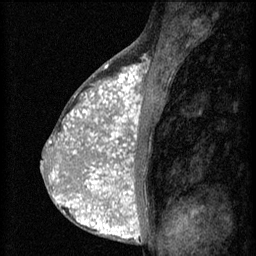
Breast MRI (dynamic contrast-enhanced), one sagittal slice. 3 images stored at this slice position (order not interpretable as contrast timing). 1.5 T. TE 4.2 ms, TR 8.2 ms. 2 mm slice thickness. 256 × 256 image matrix. Female patient, age 38 years.
Outlined on this slice (semi-automatically segmented with operator editing):
- analysis volume of interest (the breast-tissue region the enhancement analysis was run in; not a lesion): bounding box [x1, y1, x2, y2] px = [92, 112, 152, 171]
- tumour enhancement mask (voxels above the 70 % enhancement threshold inside the analysis volume of interest): [92, 112, 141, 171]